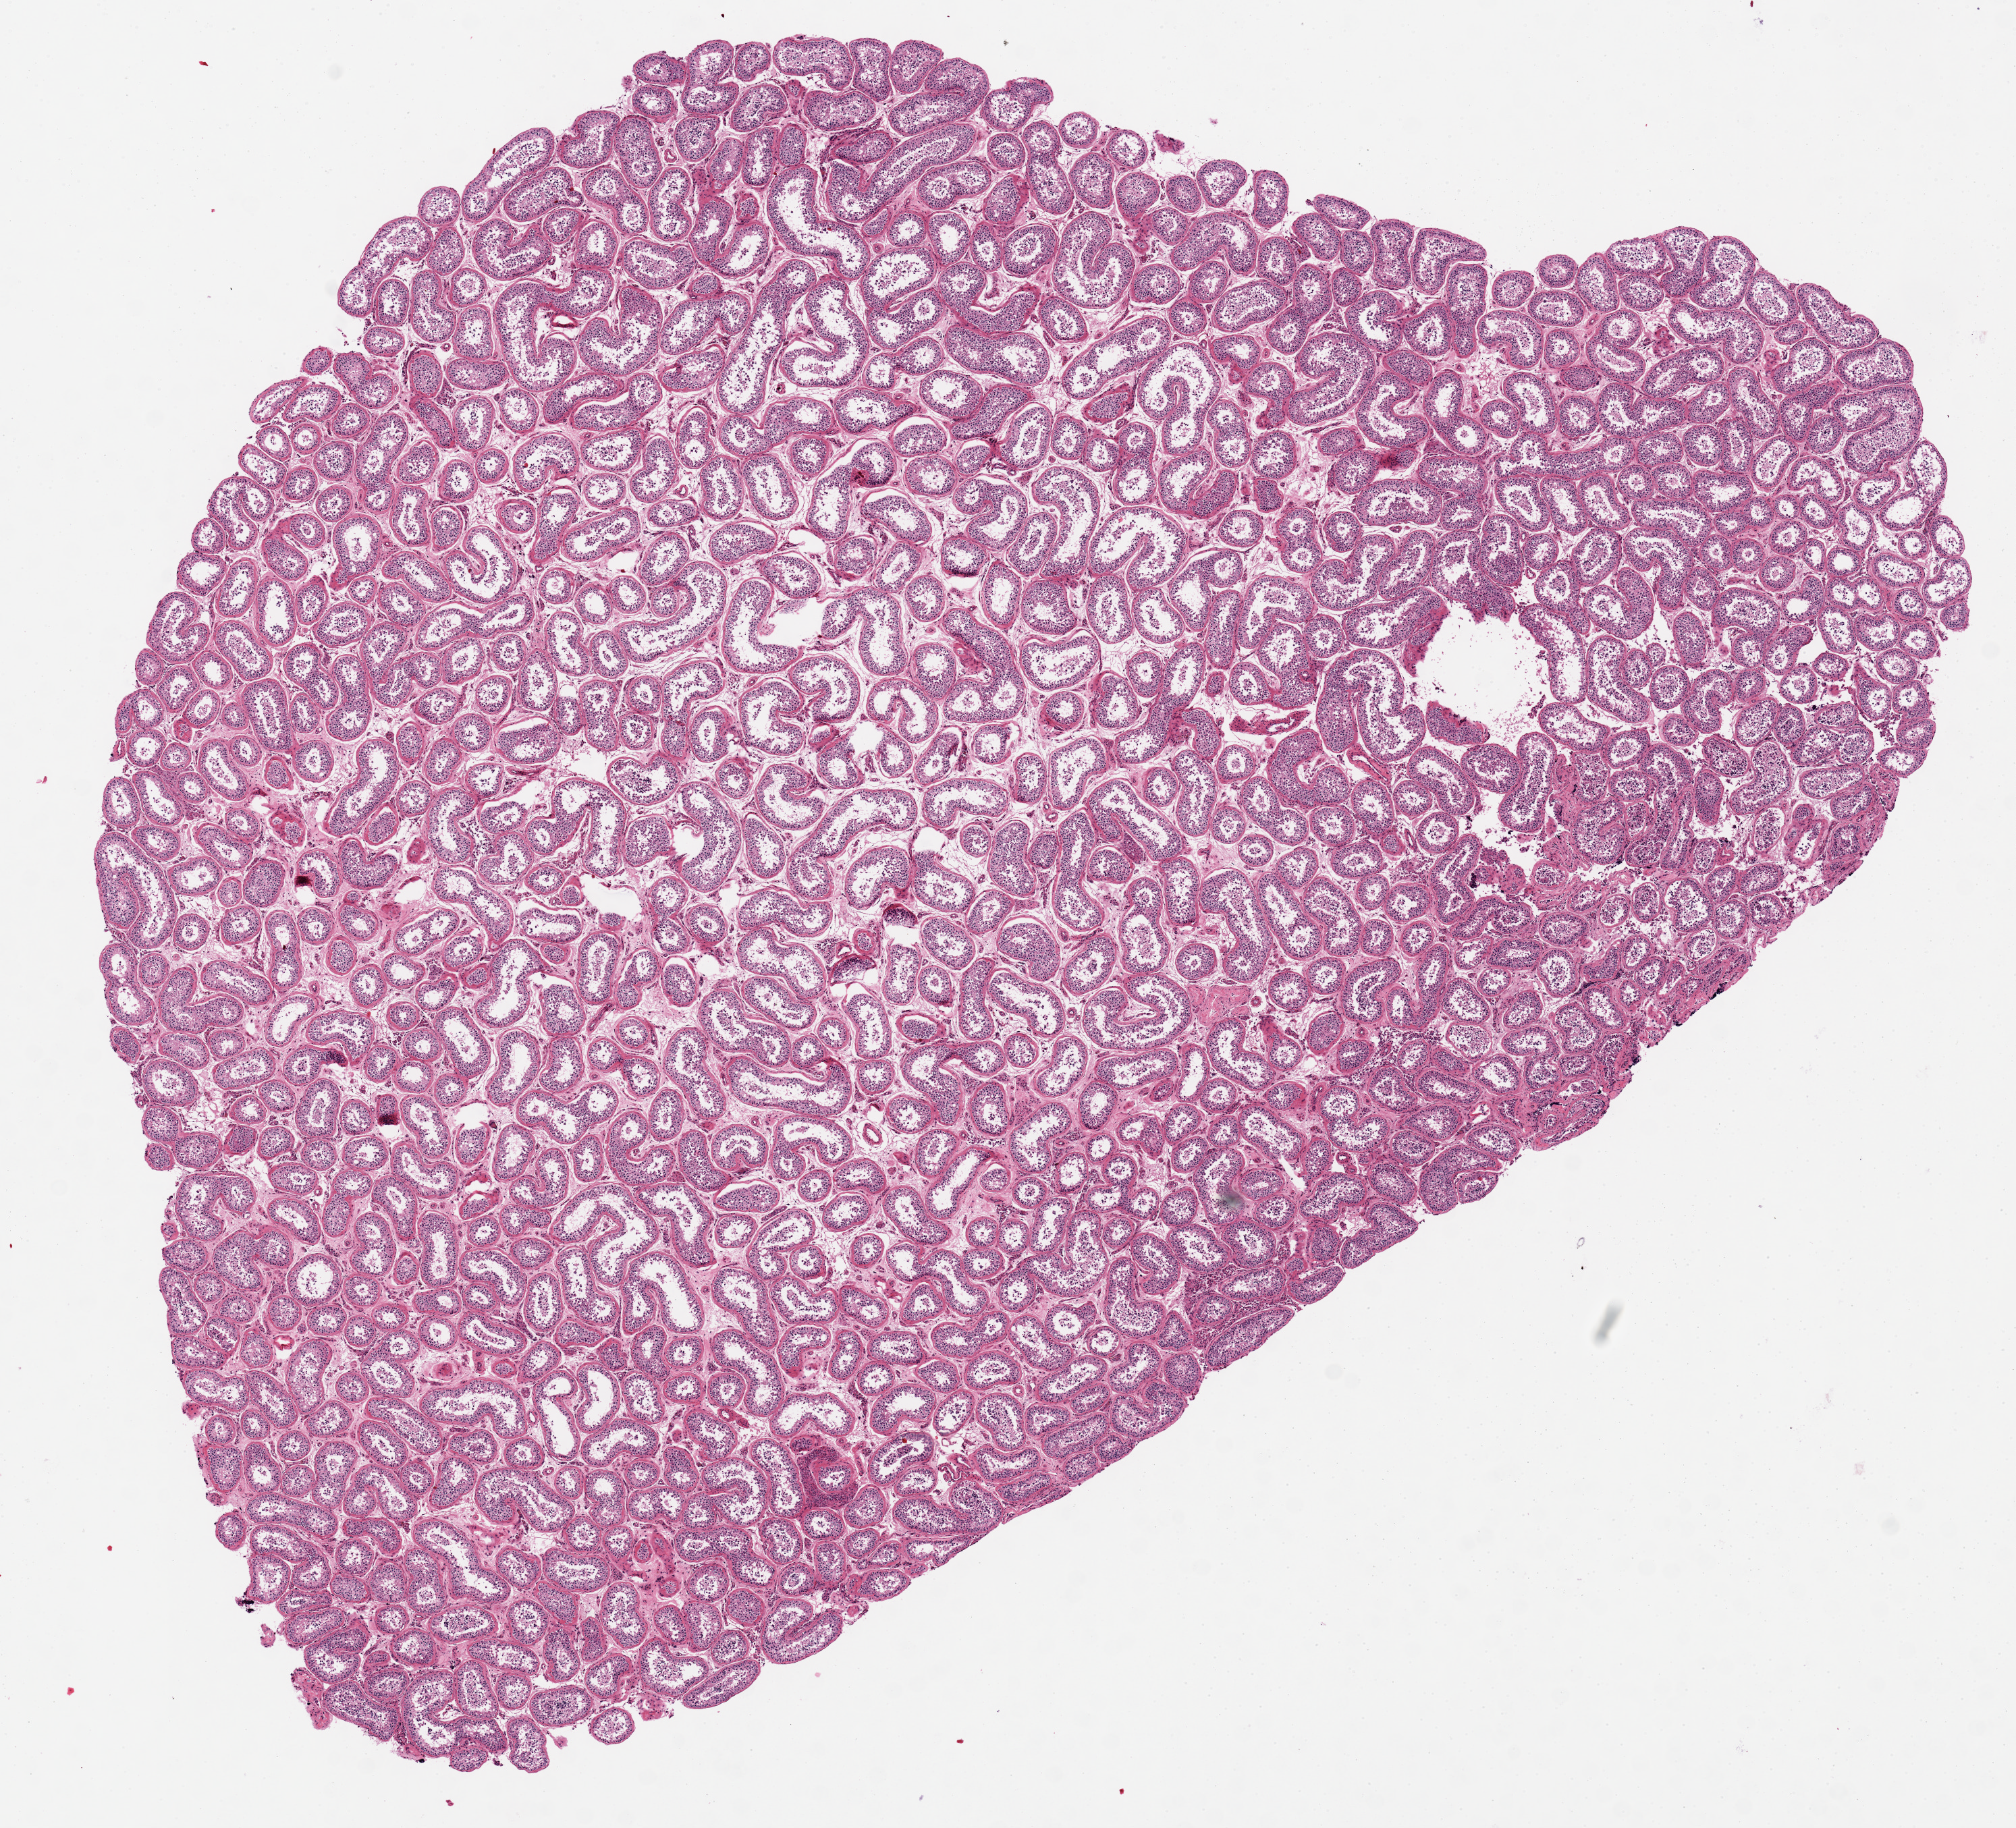
Digitized H&E-stained section — shown as a low-resolution overview of the whole scanned area (about 11.8 x 10.7 mm, acquisition: 20x scan); PAXgene-fixed, paraffin-embedded tissue; sampled site (target tissue): testis; donor tissue sample. Donor sex: male.
• pathologist's review note for this sample: Spermatogenesis. 12x8mm